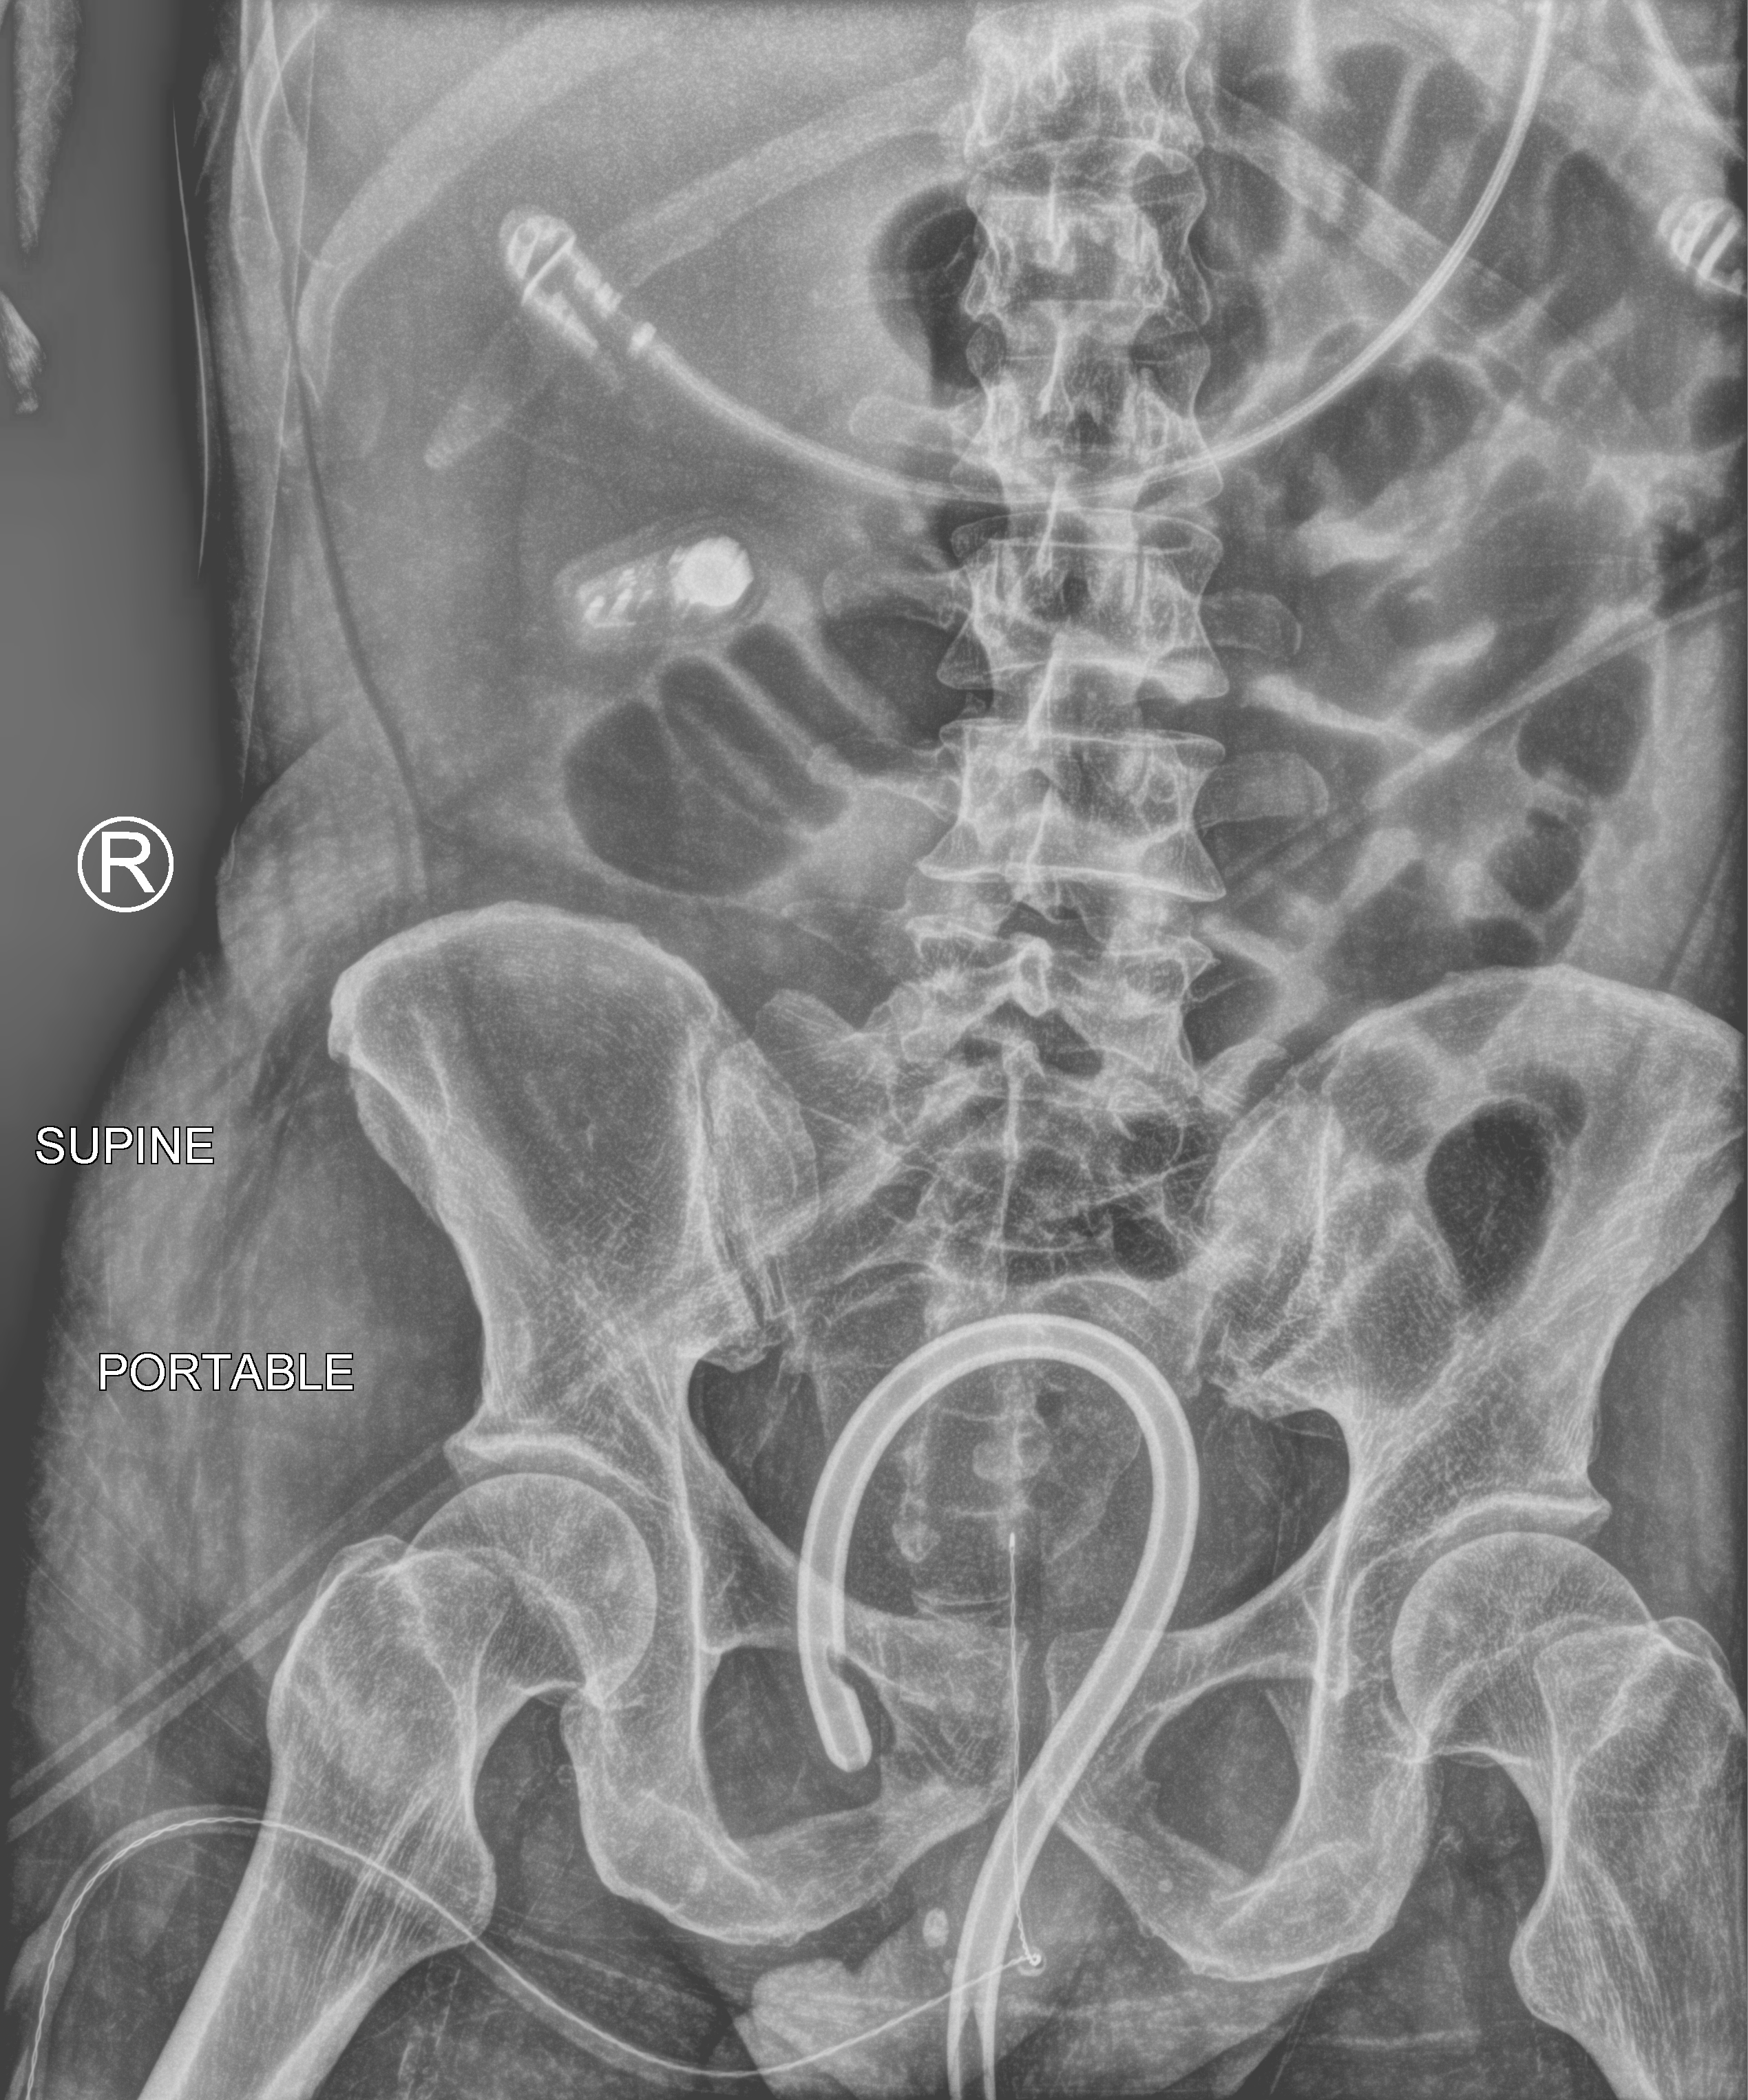
Abdomen X-ray (portable). Male patient hospitalised with COVID-19, age 18–59 years.
Admission-level facts for this patient (not findings on this image; timing relative to this image not recorded):
- admitted to intensive care during this hospital stay: yes
- mechanically ventilated during this hospital stay: yes